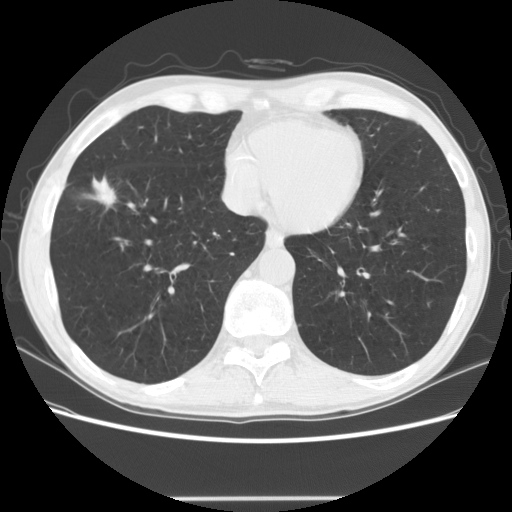
Low-dose screening chest CT, one axial slice. Slice 50 of 145 in the series (ordered by position). Lung window (W 1500 / L -600 HU). 2.5 mm slice thickness. 512 × 512 image matrix, field of view 365 × 365 mm.
Structures marked on this image (expert manual segmentation):
- lesion 1 (tumor, middle lobe of right lung): bounding box [x1, y1, x2, y2] px = [87, 176, 117, 210]